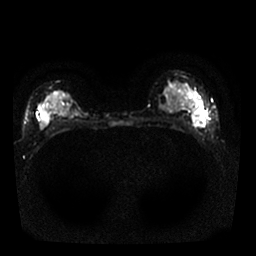
Breast MRI, one axial slice. Position 12 of 25 along the scan axis. Diffusion-weighted series; image 2 of 4 stored at this slice position (different b-values; order by instance number). 1.5 T. 4 mm slice thickness. 256 × 256 image matrix, field of view 320 × 320 mm. Female patient.
Annotated regions visible in this slice (outlined manually by an expert reader):
- tumour on diffusion-weighted imaging: bounding box (x1, y1, x2, y2) in pixels: (191, 110, 206, 128)